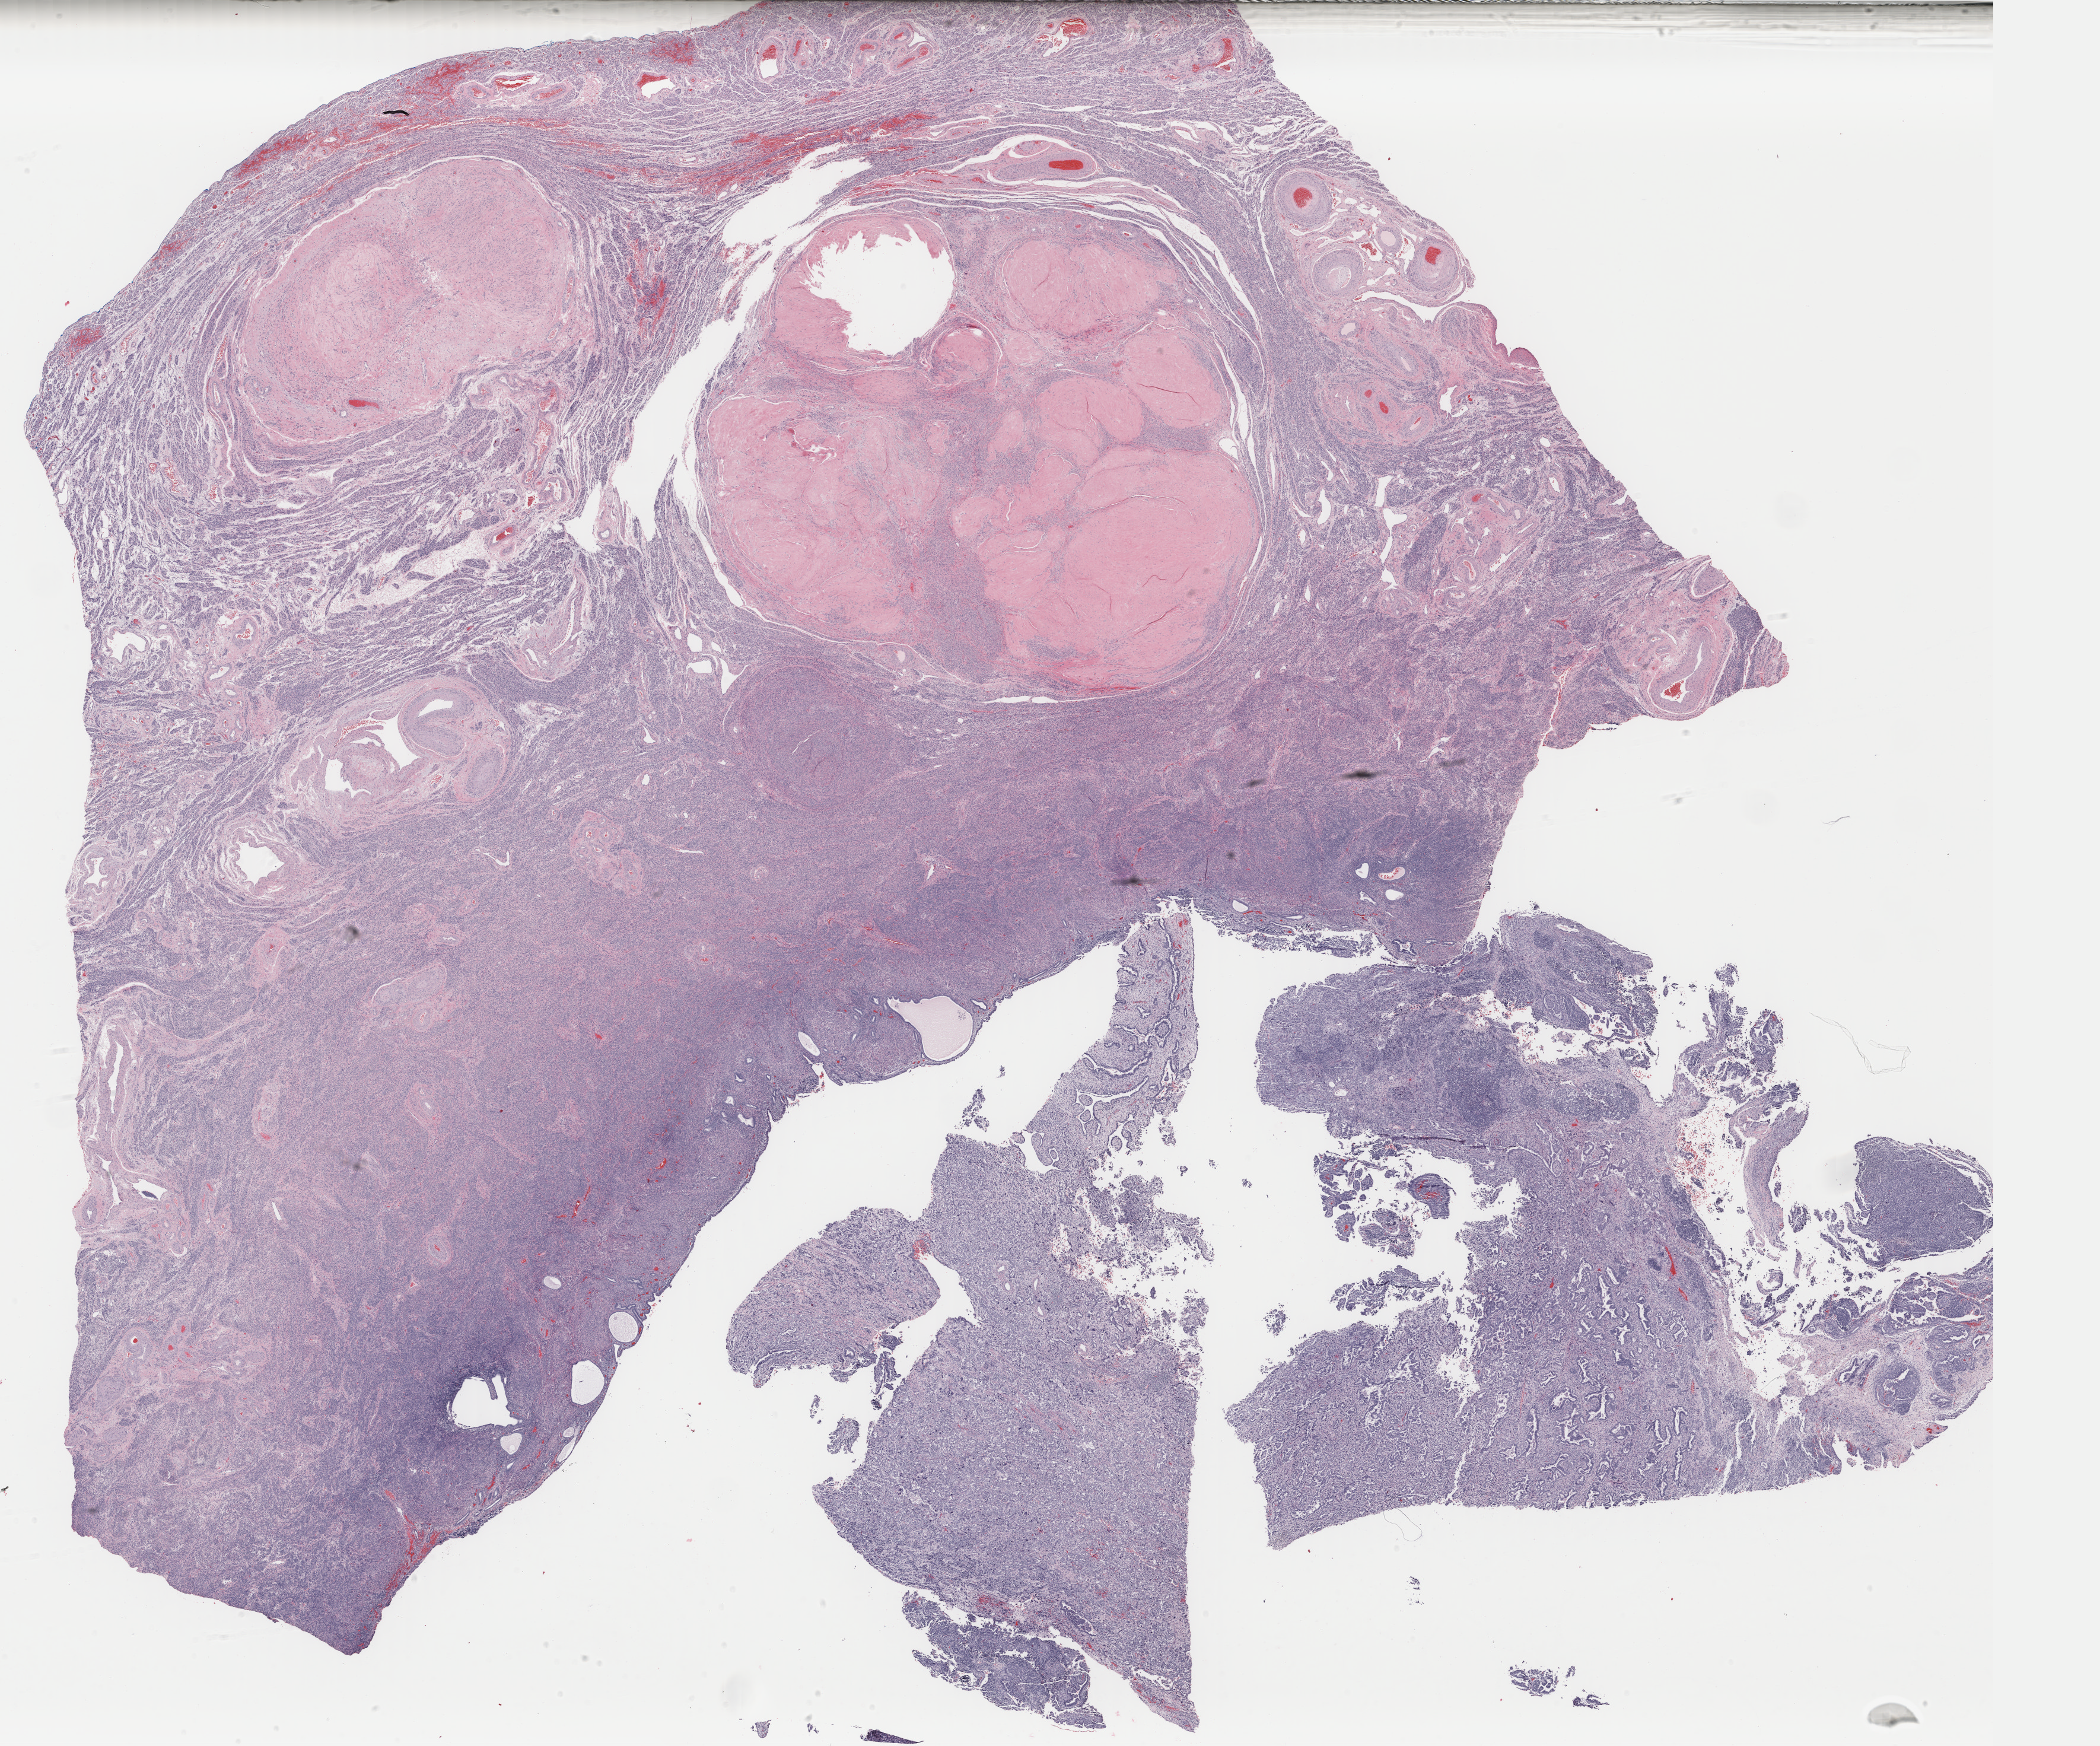
Digitized Hematoxylin and eosin (H&E) stained tissue section (whole slide), low-resolution overview of the scanned area, about 28.1 x 23.4 mm (from a 40x scan), FFPE section, primary tumour sample from the uterus. Female, age 65 years at initial diagnosis.
Histologic diagnosis: Mullerian mixed tumor.